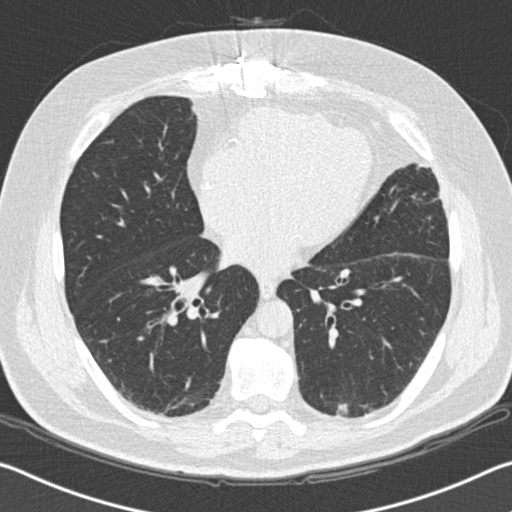
Chest CT (low-dose screening protocol), one axial image, second screening round (one year after baseline), lung window (W 1500 / L -600 HU), 2 mm slice thickness, slice 96 of 172 in the series. Male participant, aged 65 years at enrolment. Former smoker at enrolment.
• Expert-annotated lung lesion, bounding box <323,386,382,436> (left, top, right, bottom; pixels).
• Screening reader's record for this exam (one nodule recorded; not confirmed to be the boxed lesion): non-calcified nodule or mass ≥4 mm, left lower lobe, 19 × 11 mm, spiculated (stellate) margins, soft tissue attenuation, pre-existing on the prior screen: yes; interval growth: yes.
• Official screen result: positive, change unspecified: nodule(s) >= 4 mm or enlarging nodule(s), mass(es), or other non-specific abnormalities suspicious for lung cancer.